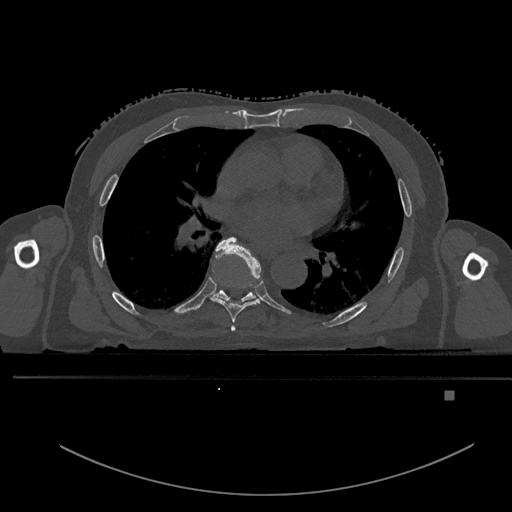
CT including the spine, one axial slice. Position 286 of 969 along the scan axis. Bone window (W 1800 / L 400 HU). 0.5 mm slice thickness. 512 × 512 image matrix, field of view 456 × 456 mm. Patient: male, 82 years. From the clinical record (not read from this slice): primary cancer: prostate.
Outlined on this slice (semi-automatic segmentation, software-assisted and operator-edited):
- T5 vertebra: box from (x=231, y=326) to (x=236, y=331) px
- T6 vertebra: (x=211, y=237)–(x=261, y=323)
- T7 vertebra: (x=214, y=290)–(x=256, y=301)